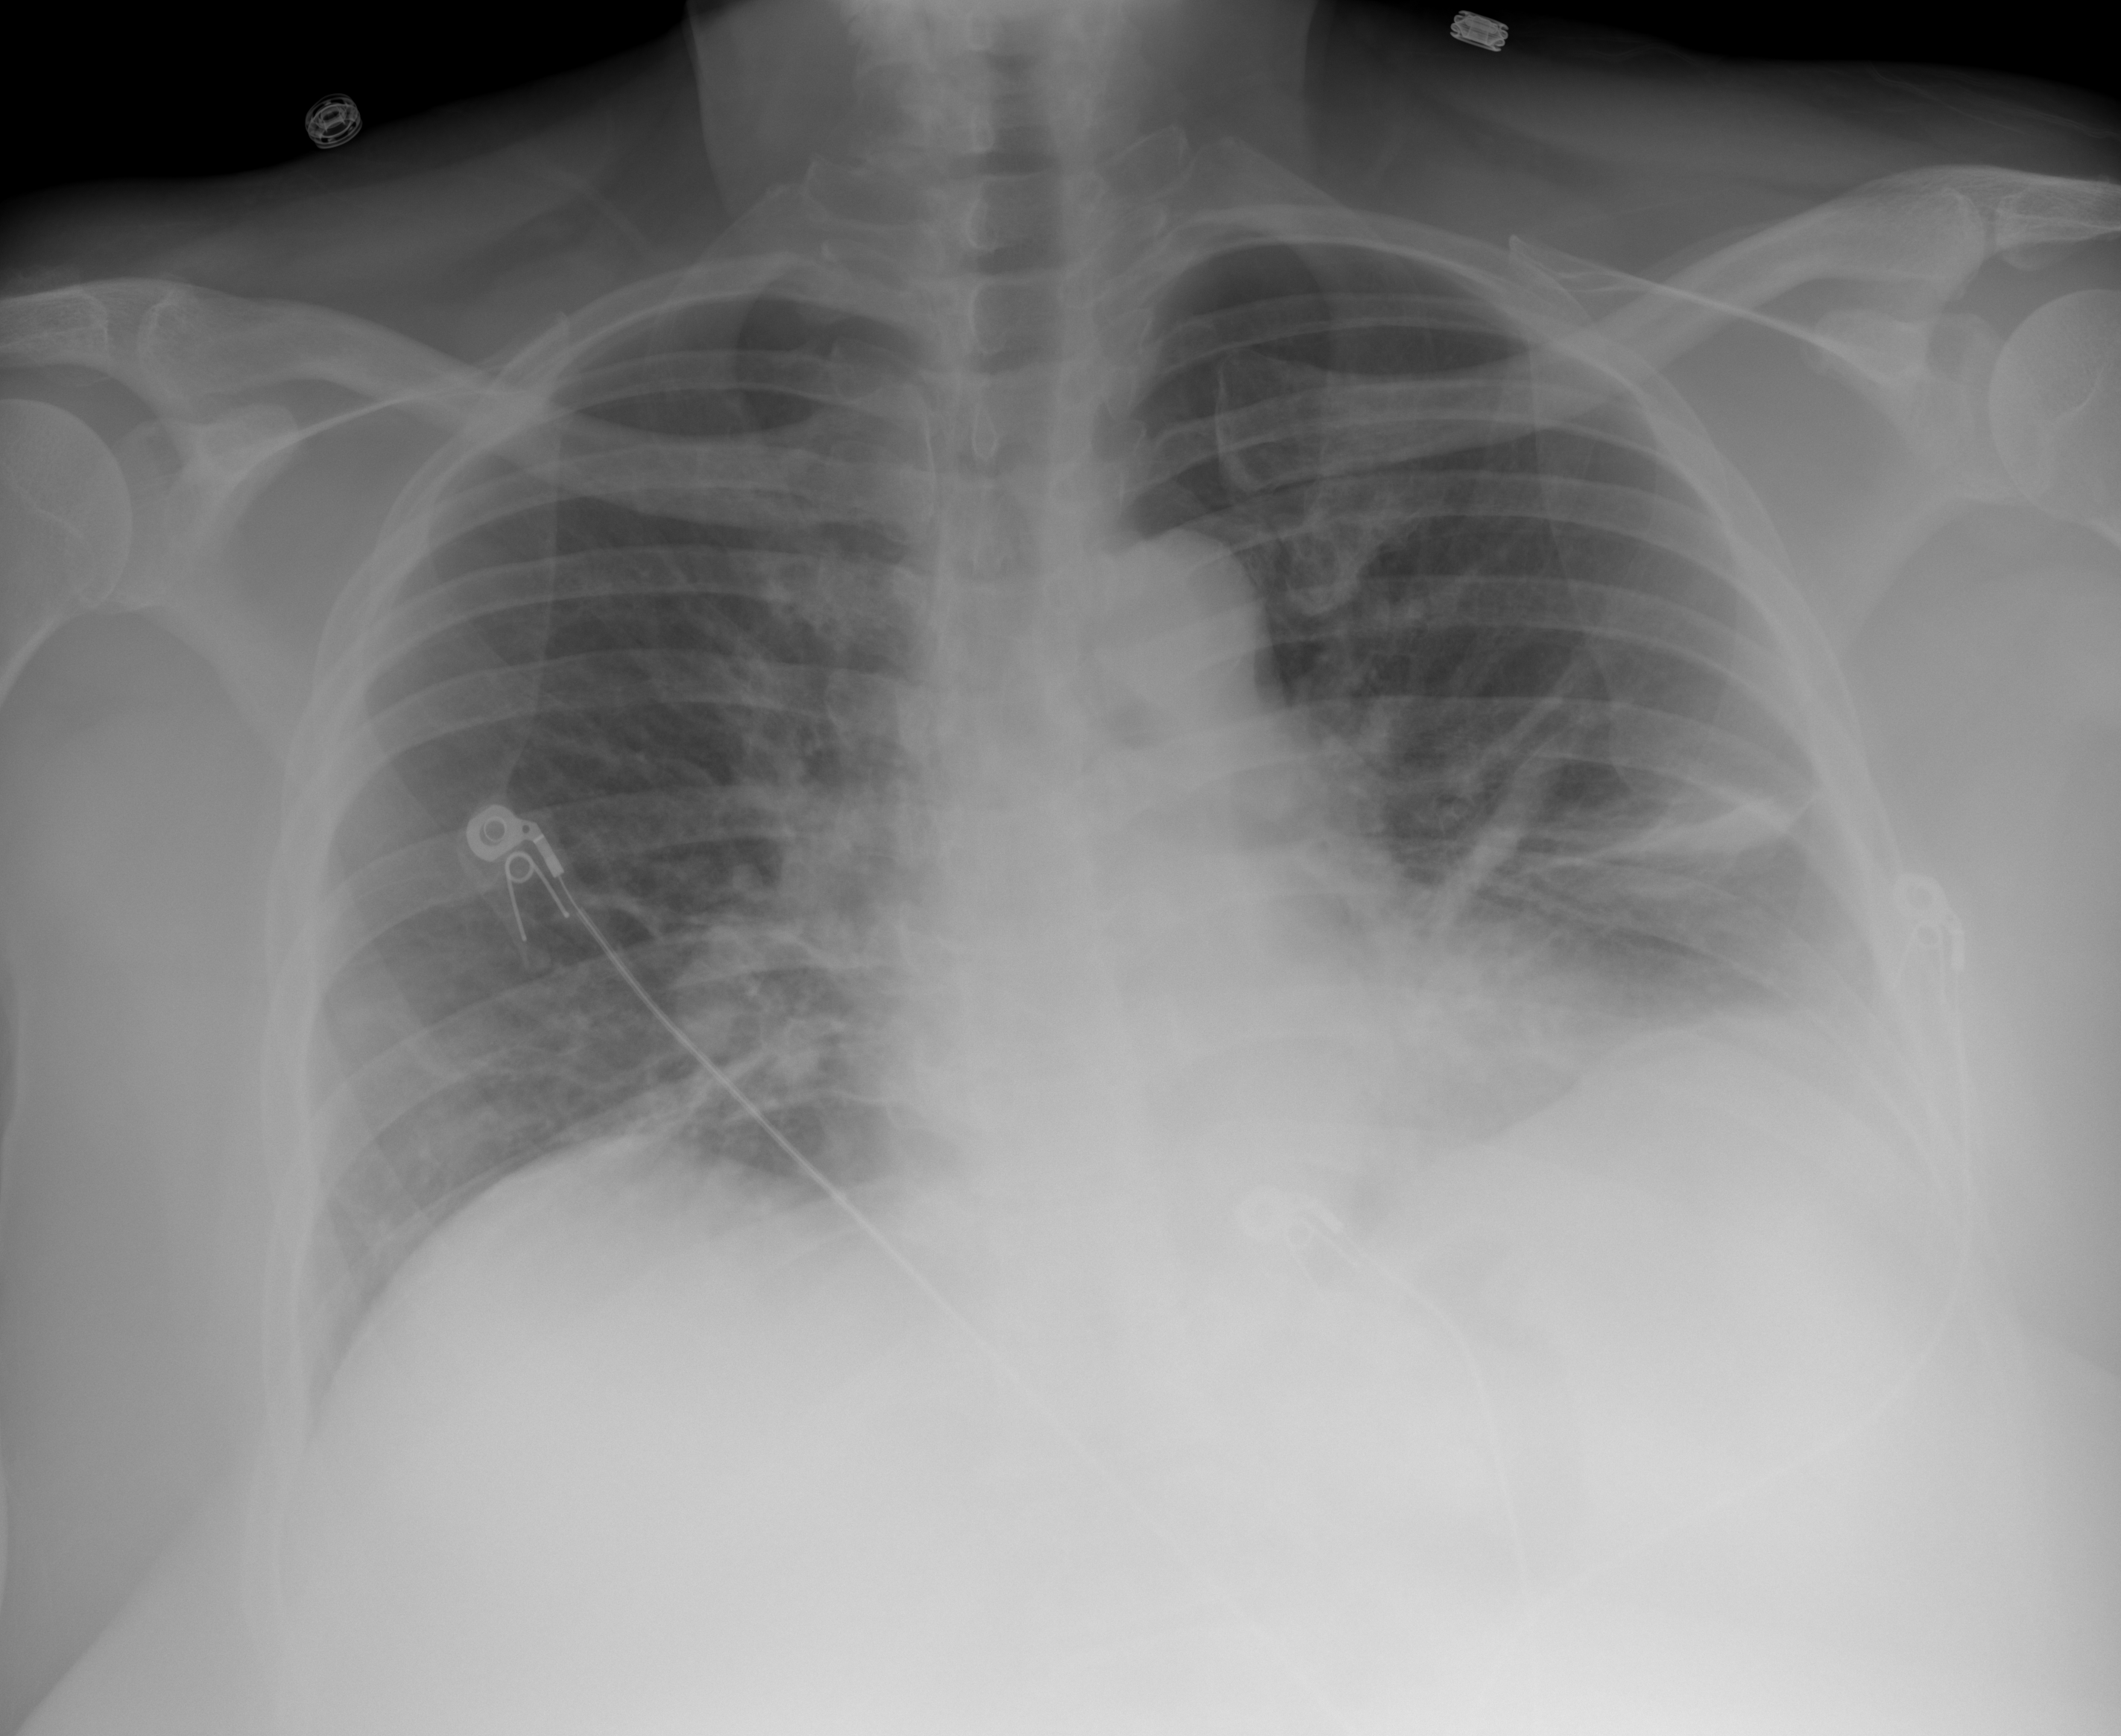
Portable chest radiograph, AP projection. Female patient, age 57 years; imaged 3 days after the COVID-19 diagnosis.
Radiologist's key findings for this exam: Patchy airspace opacity within the left lower lobe and to a lesser extent within the right lower lobe.